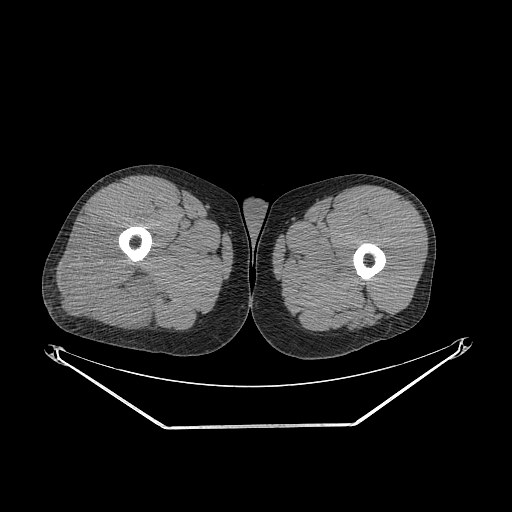
CT of an extremity soft-tissue mass (from a PET/CT study), one axial slice; 140 kVp; soft-tissue window (W 400 / L 40 HU); 3.75 mm slice thickness; 512 × 512 image matrix, field of view 500 × 500 mm. Male patient. From the clinical record (not read from this slice): histological type: poorly differentiated synovial sarcoma; grade: high; site of the primary tumour: right buttock.
Structures marked on this image (expert contour drawn on MRI and transferred to this co-registered scan by the dataset authors):
- gross tumour volume including surrounding oedema: bounding box [x1, y1, x2, y2] px = [57, 217, 156, 328]
- gross tumour volume (mass): [57, 217, 156, 328]